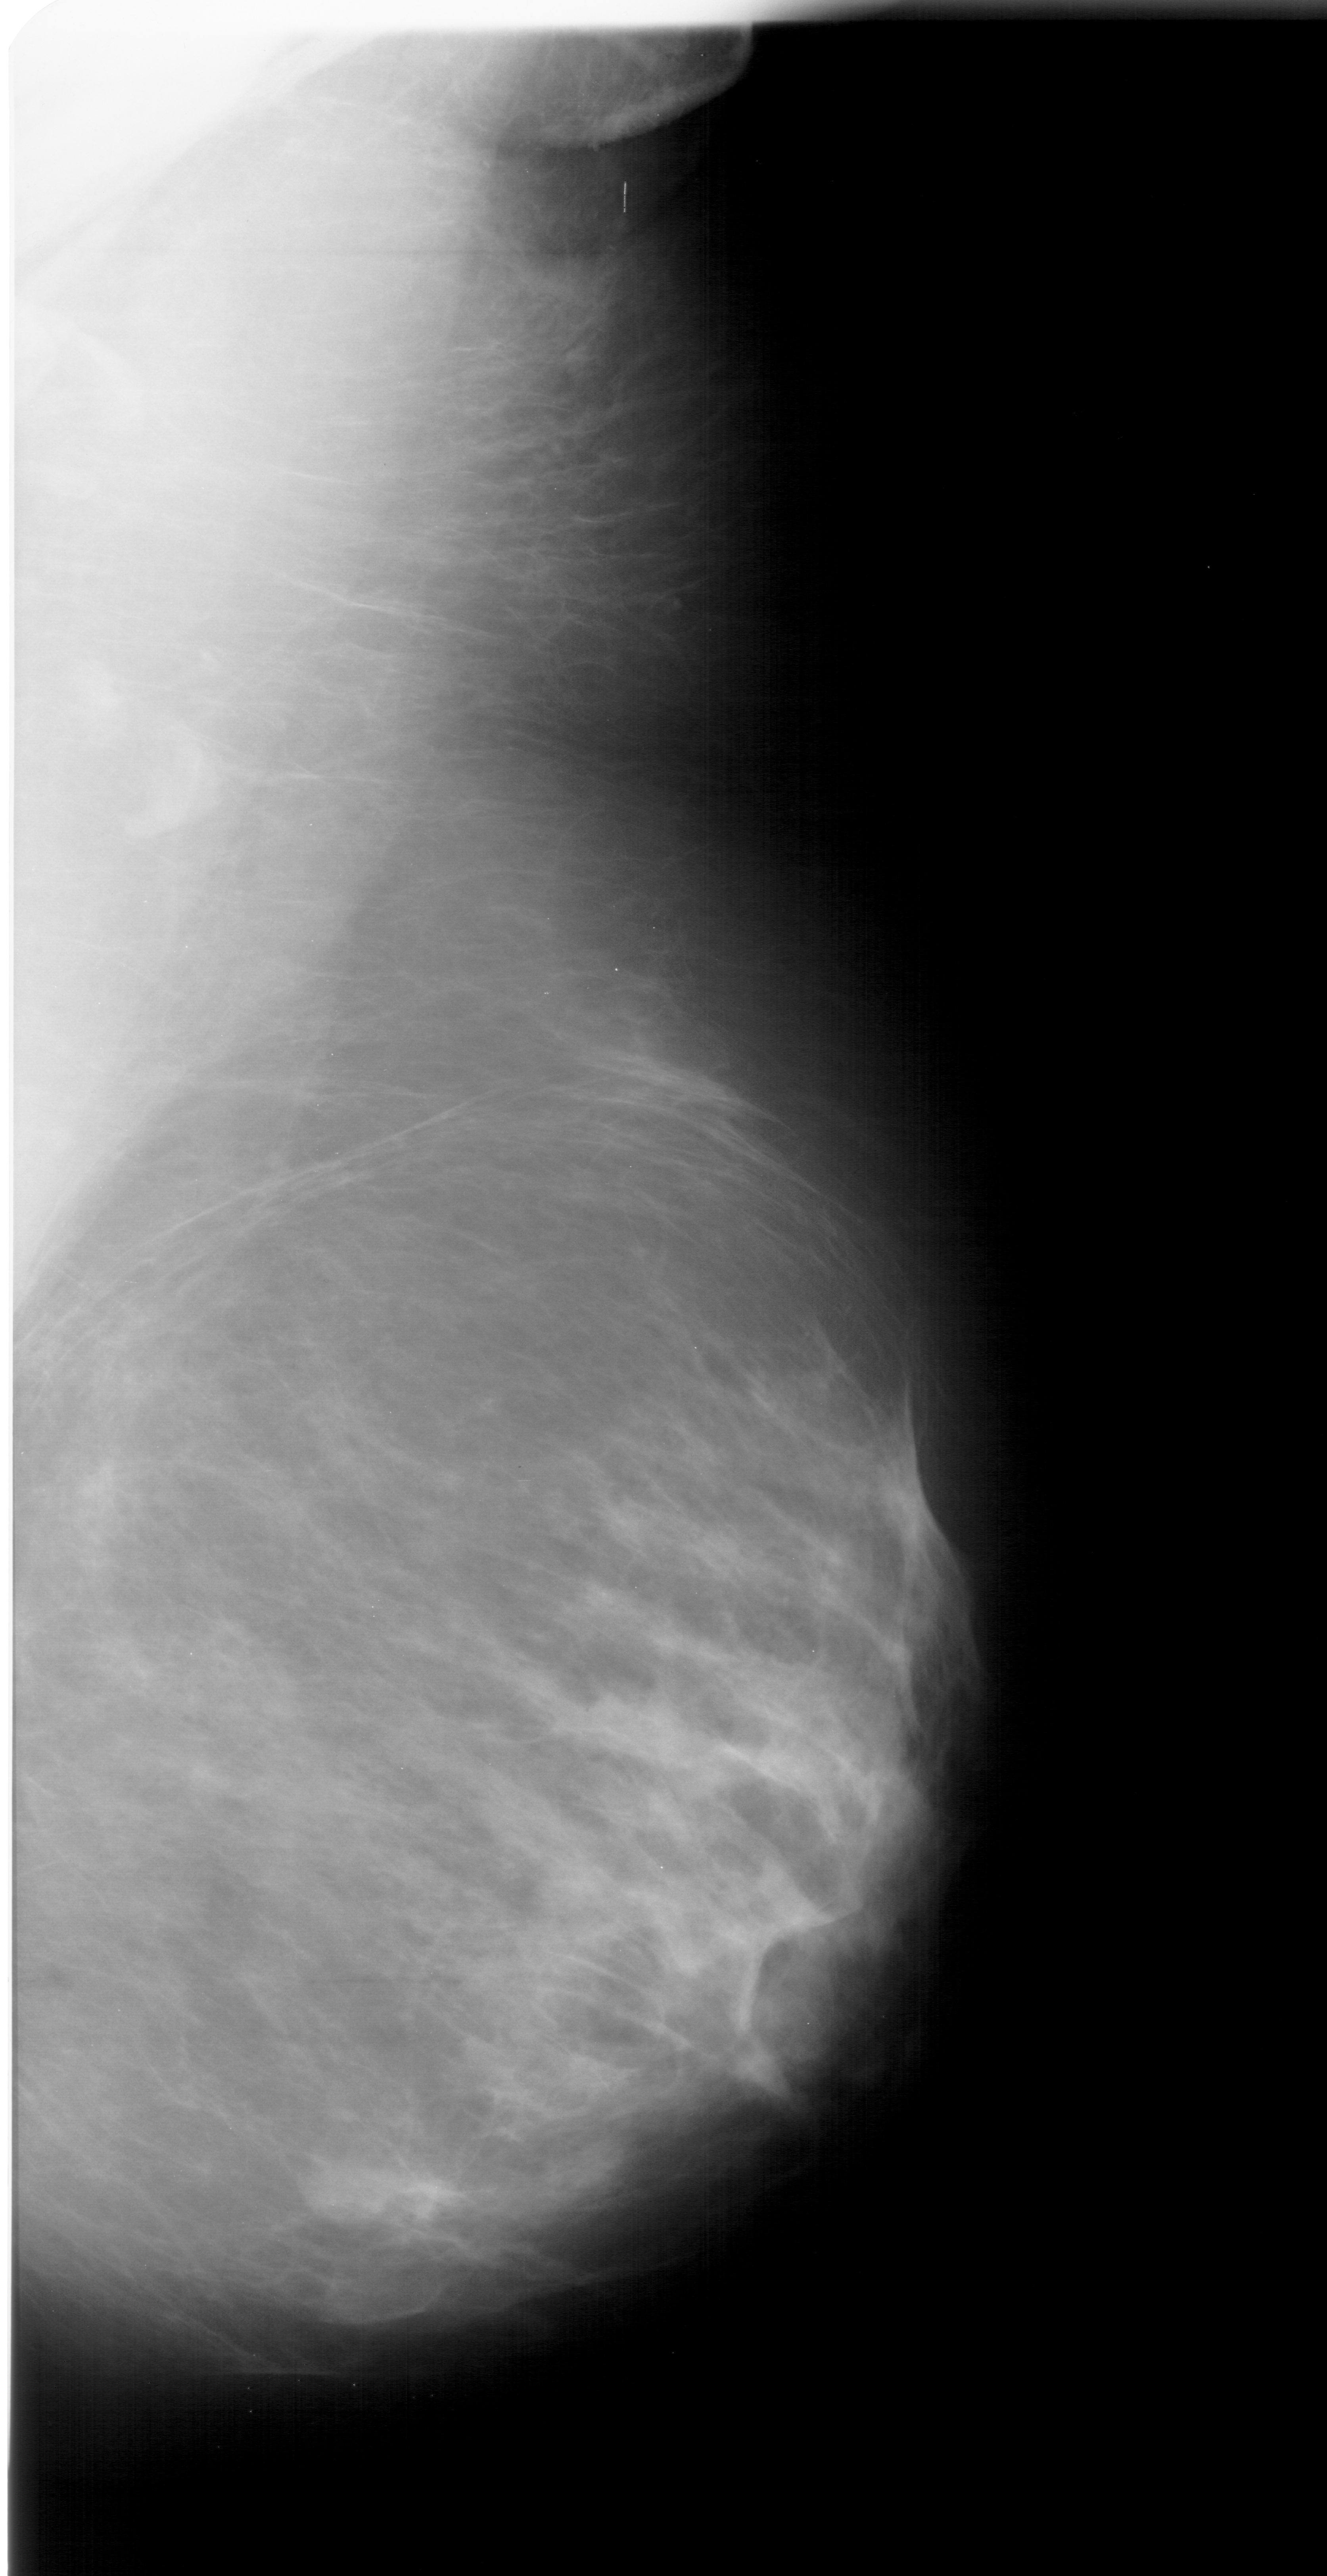
Mammogram (digitized film); right breast; mediolateral oblique (MLO) view; BI-RADS breast density category 2 (scale 1–4); 1327 × 2576 image matrix.
Marked abnormalities (boxes around the expert regions of interest):
- mass, shape lobulated, margins circumscribed; BI-RADS assessment category 3; pathology (as recorded): benign: bounding box <286,2145,412,2241> (left, top, right, bottom; pixels)